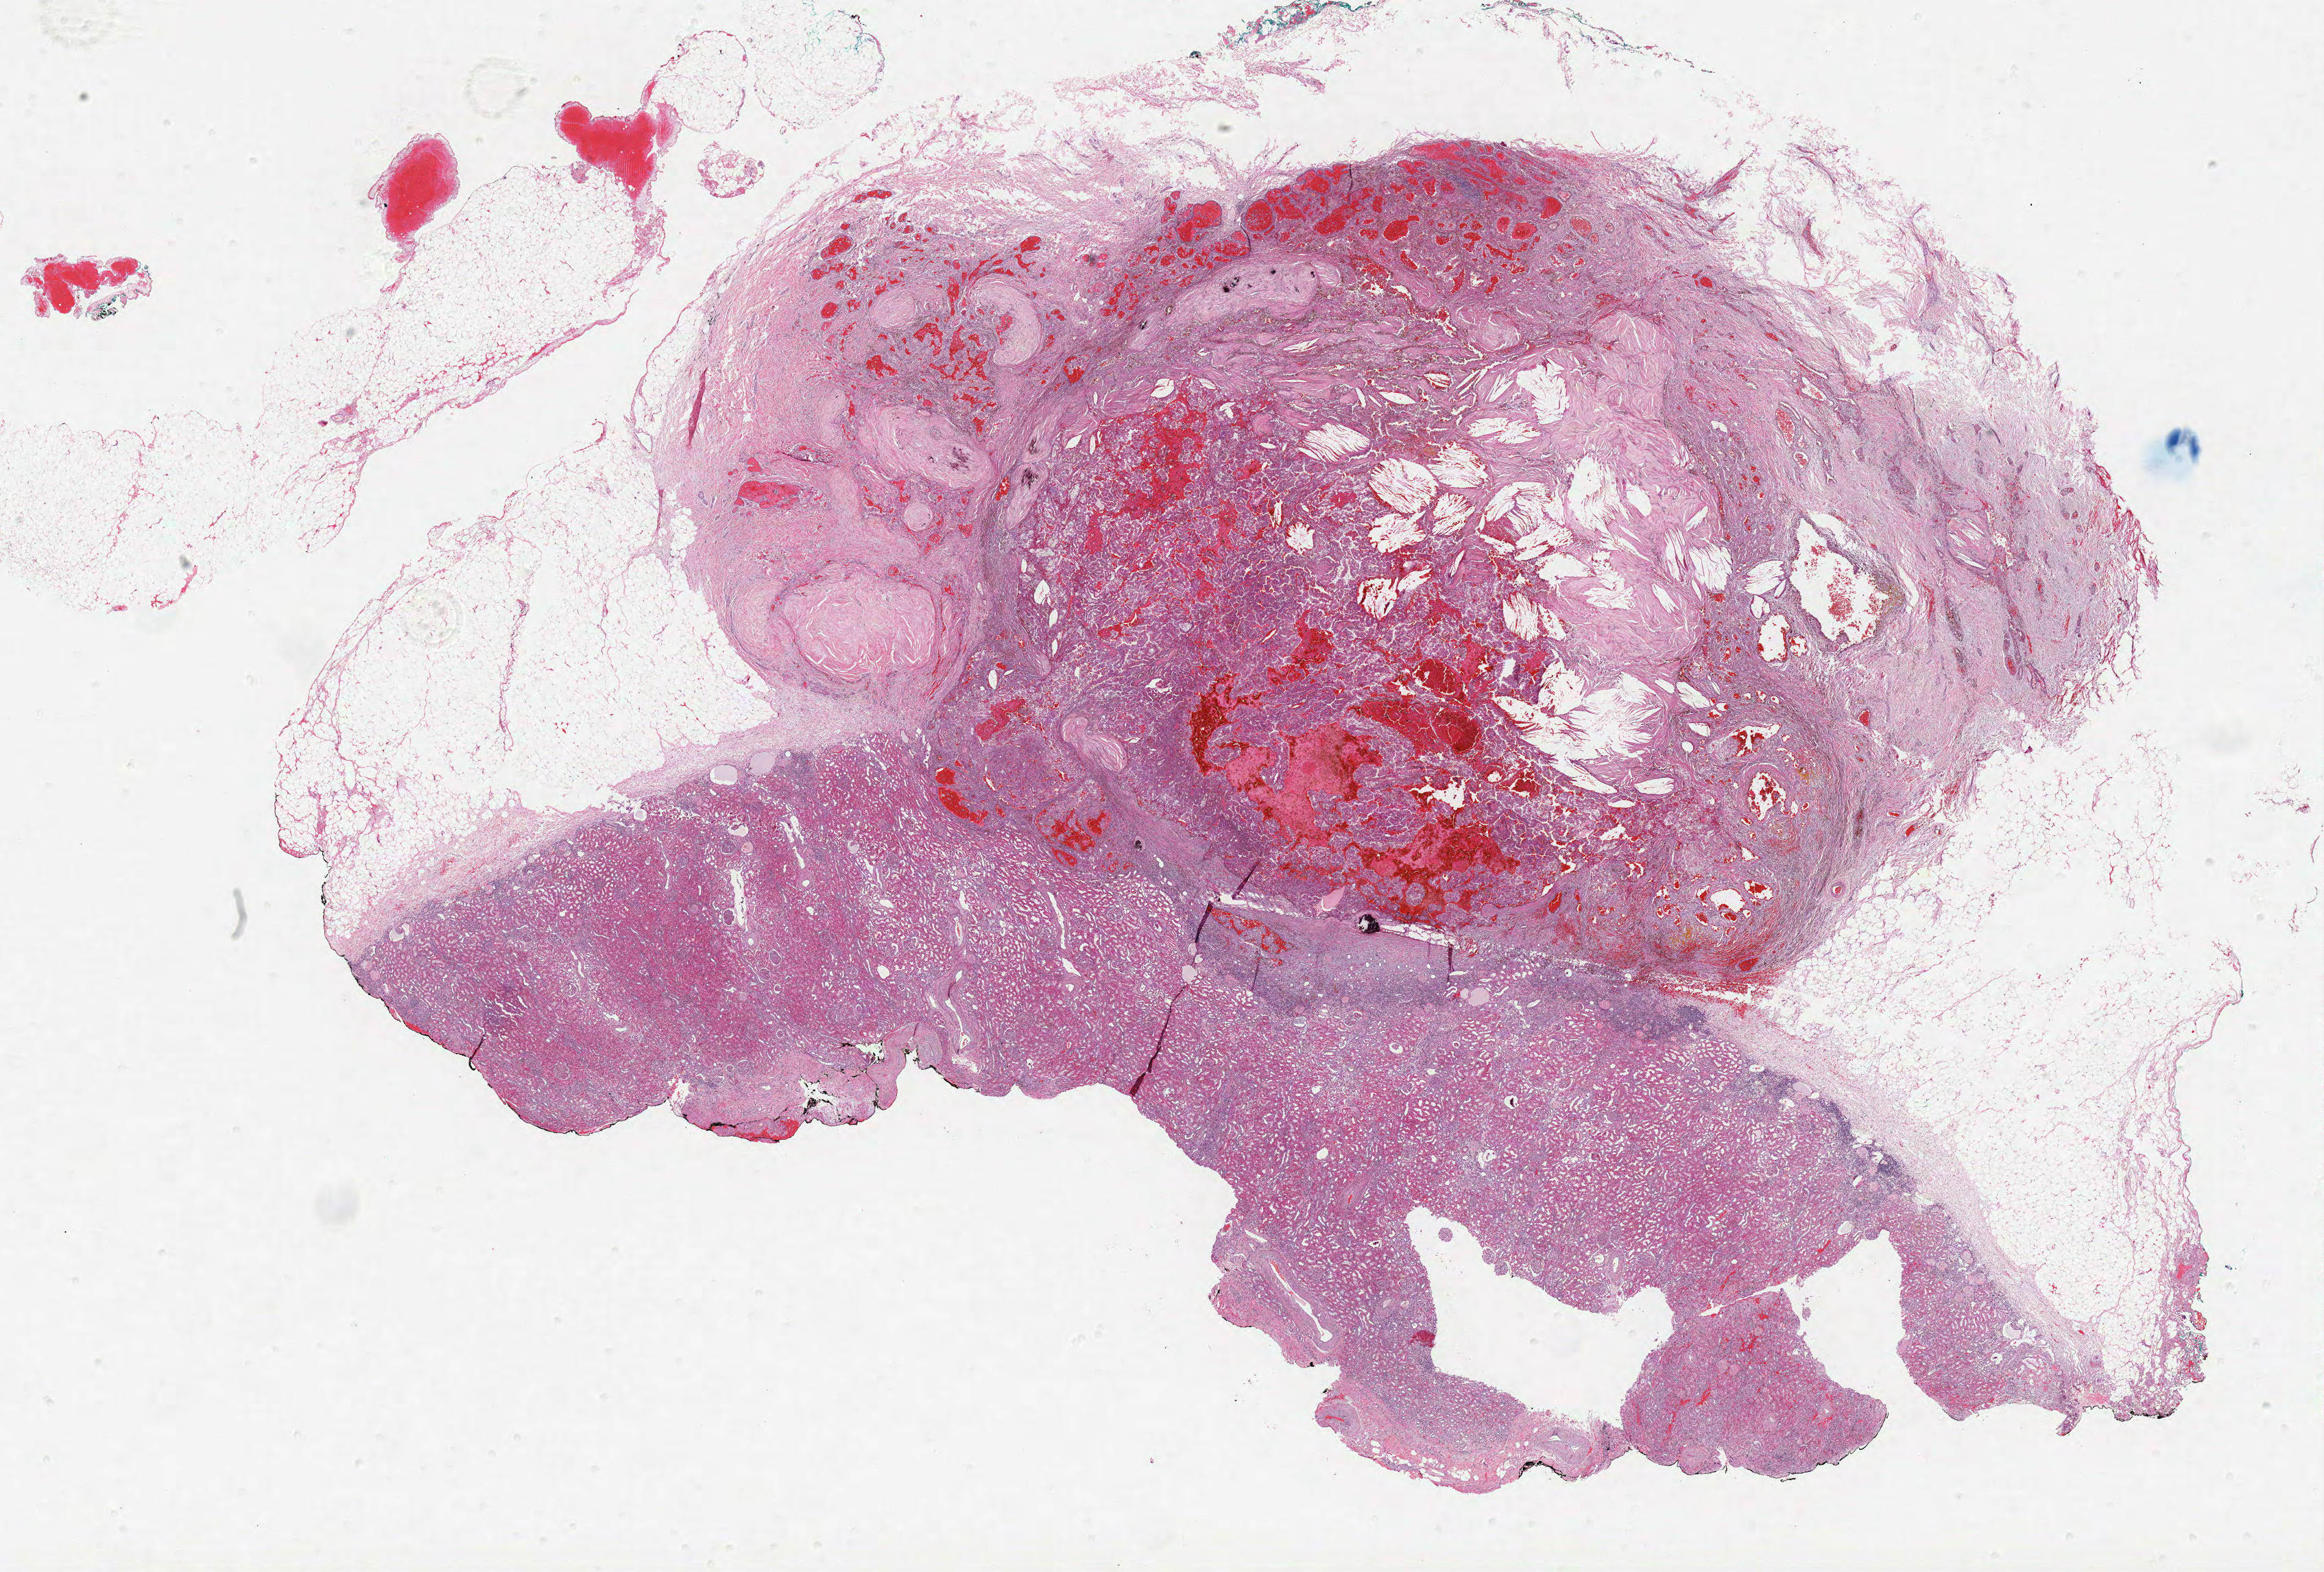
Whole-slide histology image, H&E-stained — low-resolution overview of the scanned area, about 27.1 x 18.3 mm; FFPE section; kidney, primary tumour sample. Male, age 75 years at initial diagnosis.
- pathologic diagnosis: Papillary adenocarcinoma, NOS
- AJCC pathologic stage: III